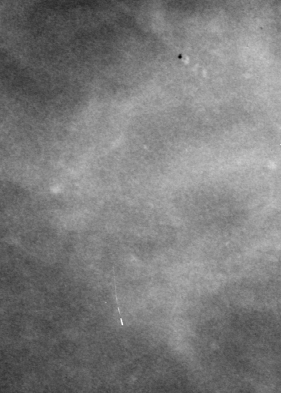
Region of interest cut from a scanned film mammogram (one marked finding), left breast, CC view, BI-RADS breast density category 3 (scale 1–4).
- Calcifications, morphology pleomorphic, distribution clustered; BI-RADS assessment category 4; subtlety rating 3 on a 1 (subtle) to 5 (obvious) scale; pathology (as recorded): benign.